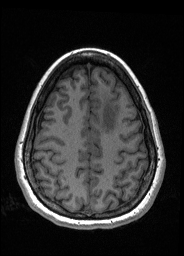
Pre-operative brain MRI before brain-tumour surgery, one axial slice; slice 57 of 176 in the series (ordered by position); T1-weighted post-contrast; 1 mm slice thickness; 184 × 256 image matrix, field of view 180 × 250 mm. From the clinical record (not read from this slice): histopathology: Oligodendroglioma; WHO grade: 2; IDH mutation: yes; tumour location: Left Frontal.
Structures marked on this image (outlined manually by an expert reader):
- tumour: bounding box <100,95,118,133> (left, top, right, bottom; pixels)